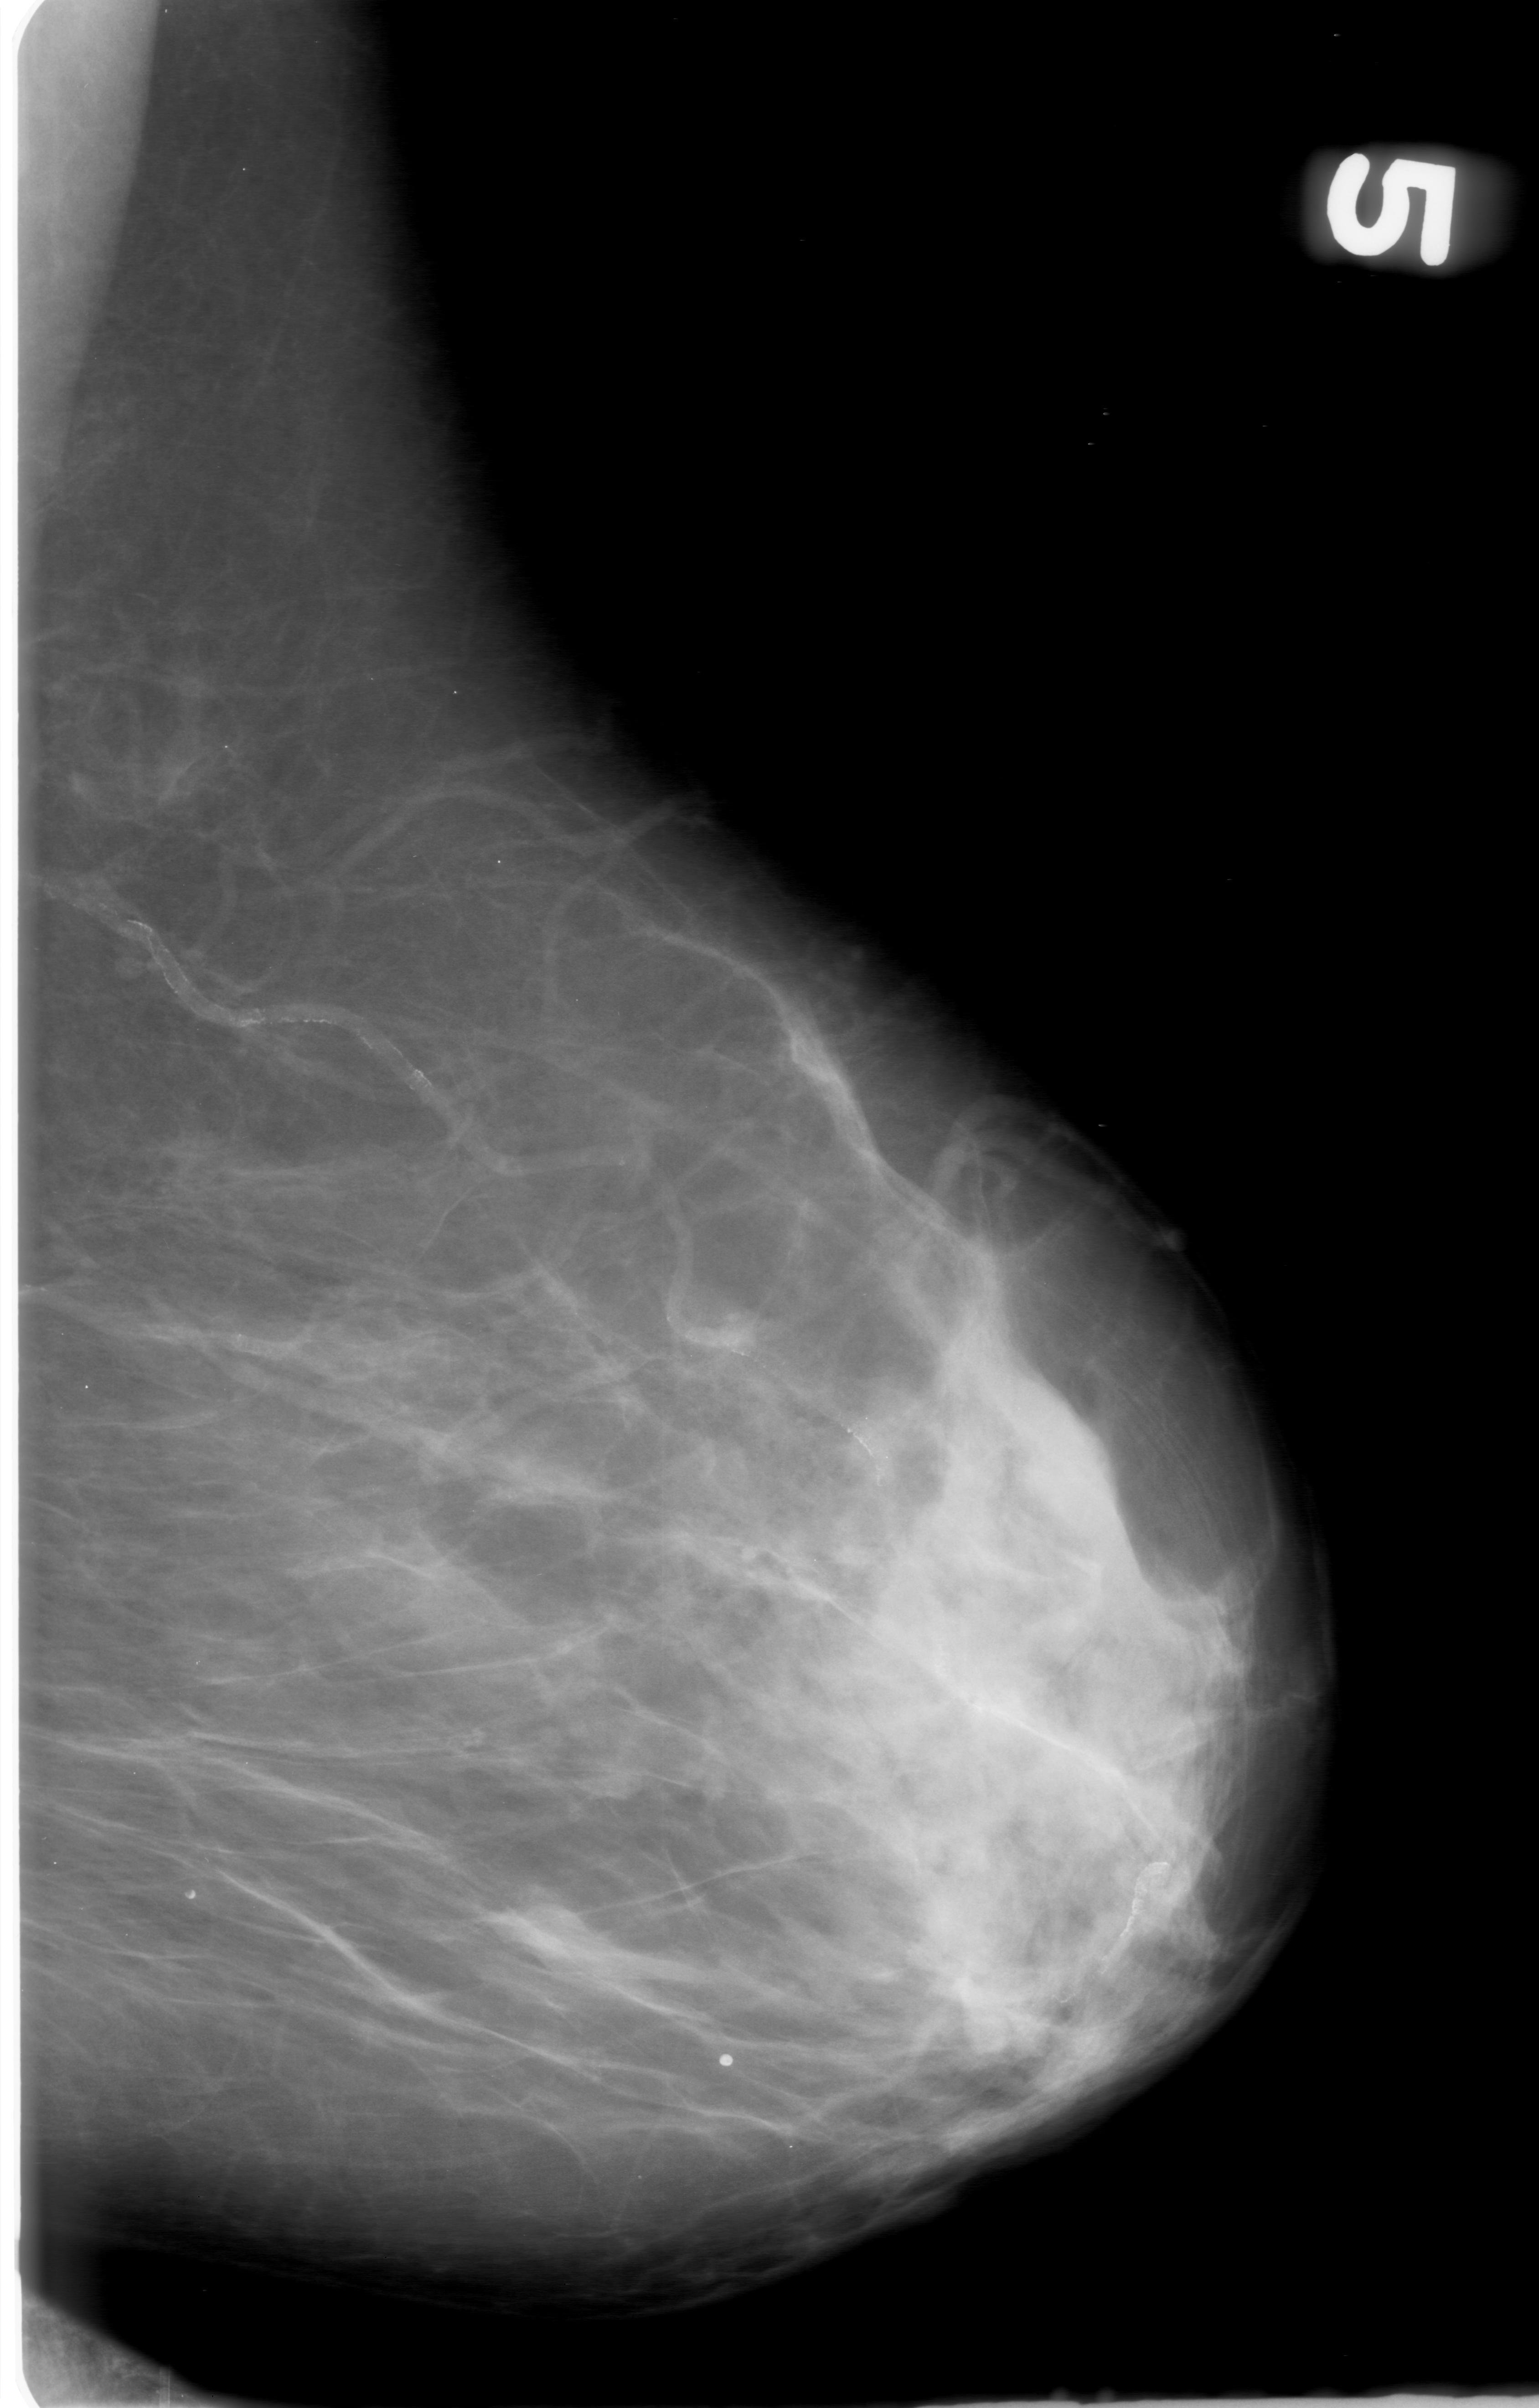
Digitized screen-film mammogram; left breast; mediolateral oblique (MLO) view; breast composition: scattered fibroglandular densities (BI-RADS density category 2 of 4); 1539 × 2408 image matrix.
Expert-marked regions of interest on this image (one box per marked abnormality):
- mass, shape round, margins obscured; BI-RADS assessment category 0; pathology result (as recorded, not read from the image): benign: bounding box (x1, y1, x2, y2) in pixels: (478, 1875, 652, 2000)